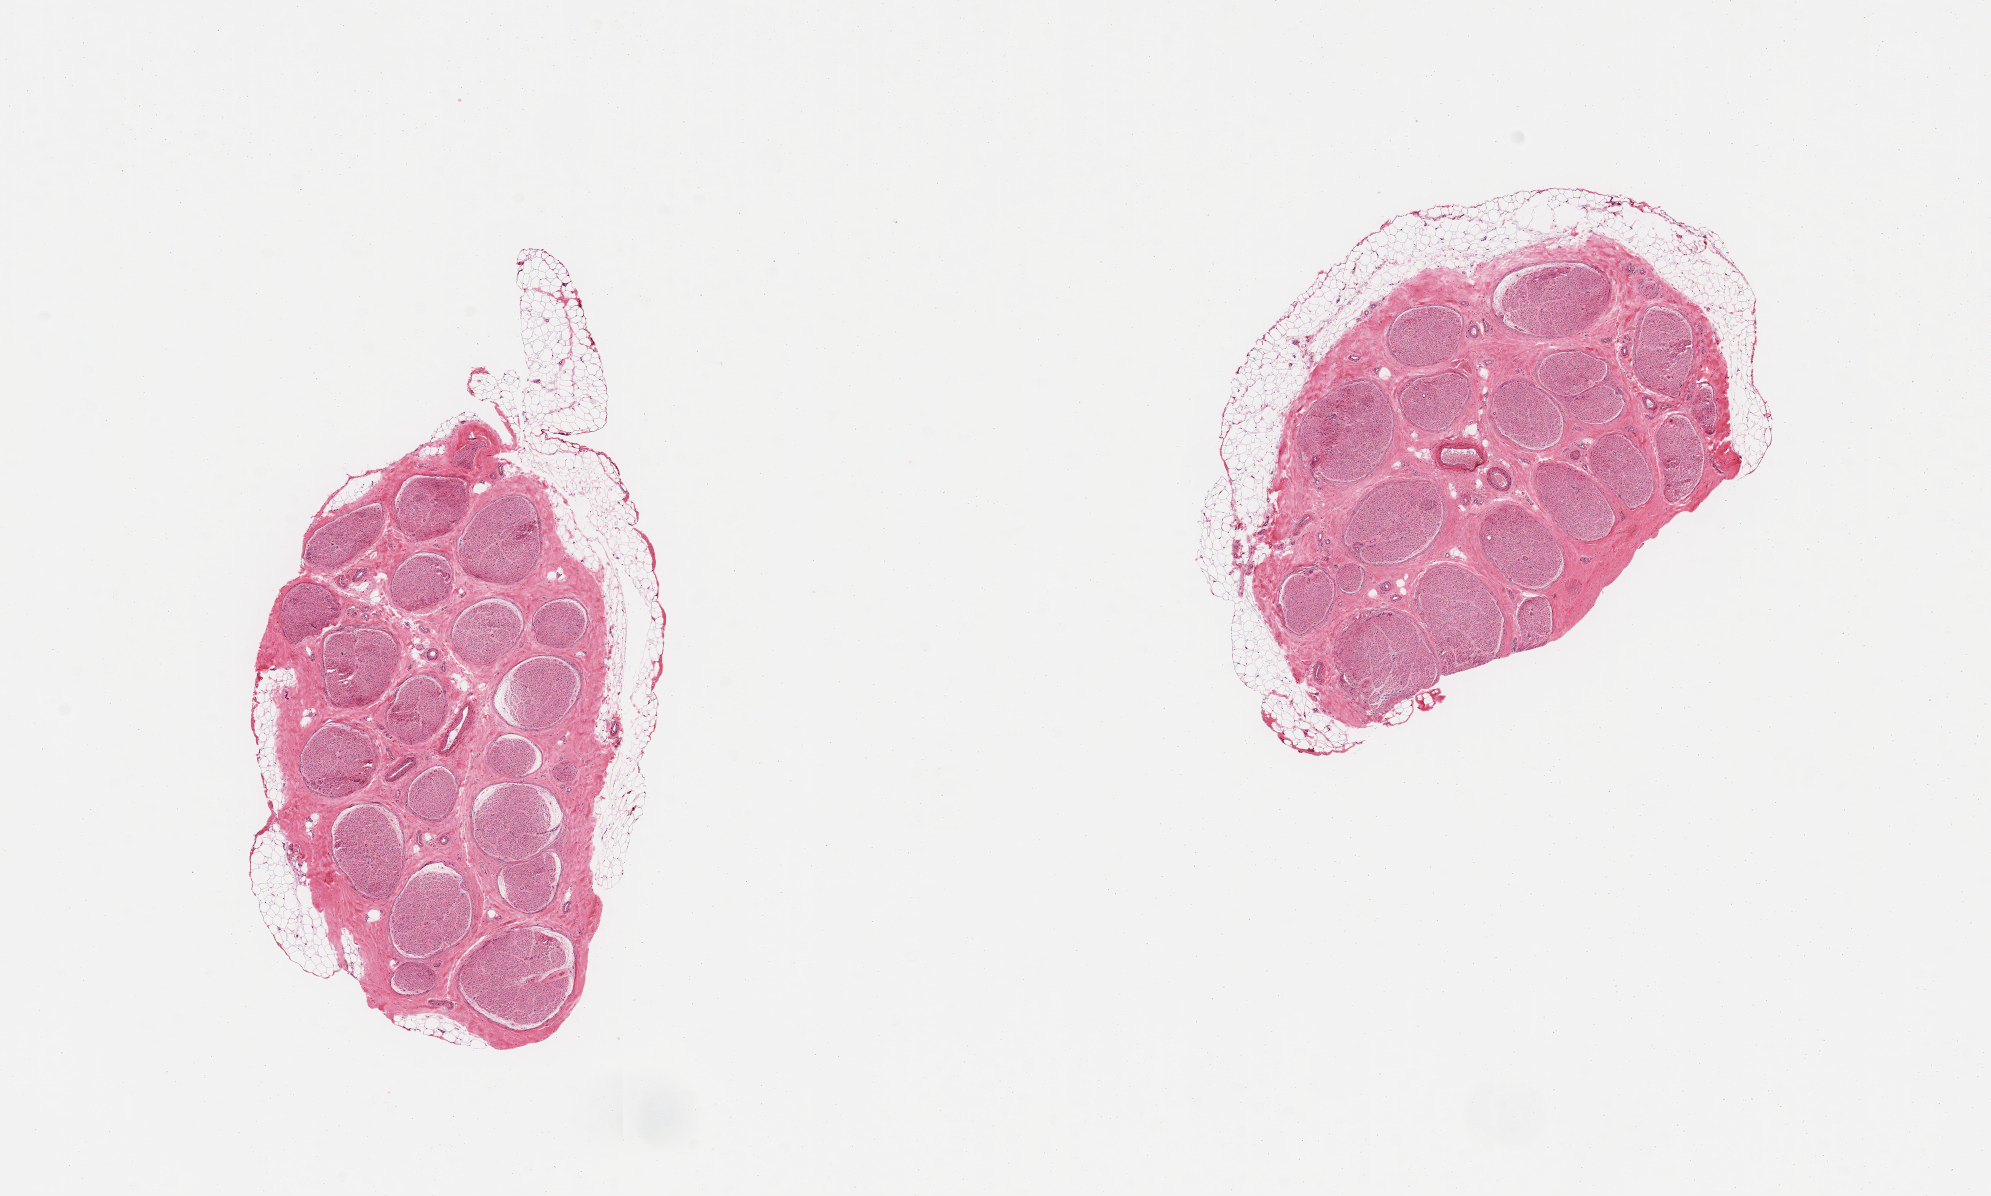
Hematoxylin and eosin (H&E) whole-slide image, brightfield, whole scanned area (about 15.8 x 9.5 mm) shown as a low-resolution overview. Donor: male.
Specimen: PAXgene-fixed, paraffin-embedded tissue; section of tibial nerve (target tissue); donor tissue sample.